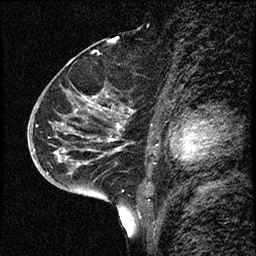
Breast MRI (dynamic contrast-enhanced), one sagittal slice; slice 38 of 68 in the series (ordered by position); dynamic contrast-enhanced study with each time point stored as its own series, time point 2 of 3 at this slice position (early post-contrast, ordered by acquisition time); 1.5 T; TE 4.2 ms, TR 17.6 ms; 2 mm slice thickness; 256 × 256 image matrix, field of view 200 × 200 mm. Female patient, age 52 years. From the clinical record (not read from this slice): setting: breast cancer imaged before/during neoadjuvant chemotherapy; receptor status: HER2-positive.
Annotated regions visible in this slice (semi-automatic segmentation, software-assisted and operator-edited):
- analysis volume of interest (the breast-tissue region the enhancement analysis was run in; not a lesion): box from (x=50, y=61) to (x=144, y=184) px
- tumour enhancement mask (voxels above the 100 % enhancement threshold inside the analysis volume of interest): (x=59, y=102)–(x=120, y=165)